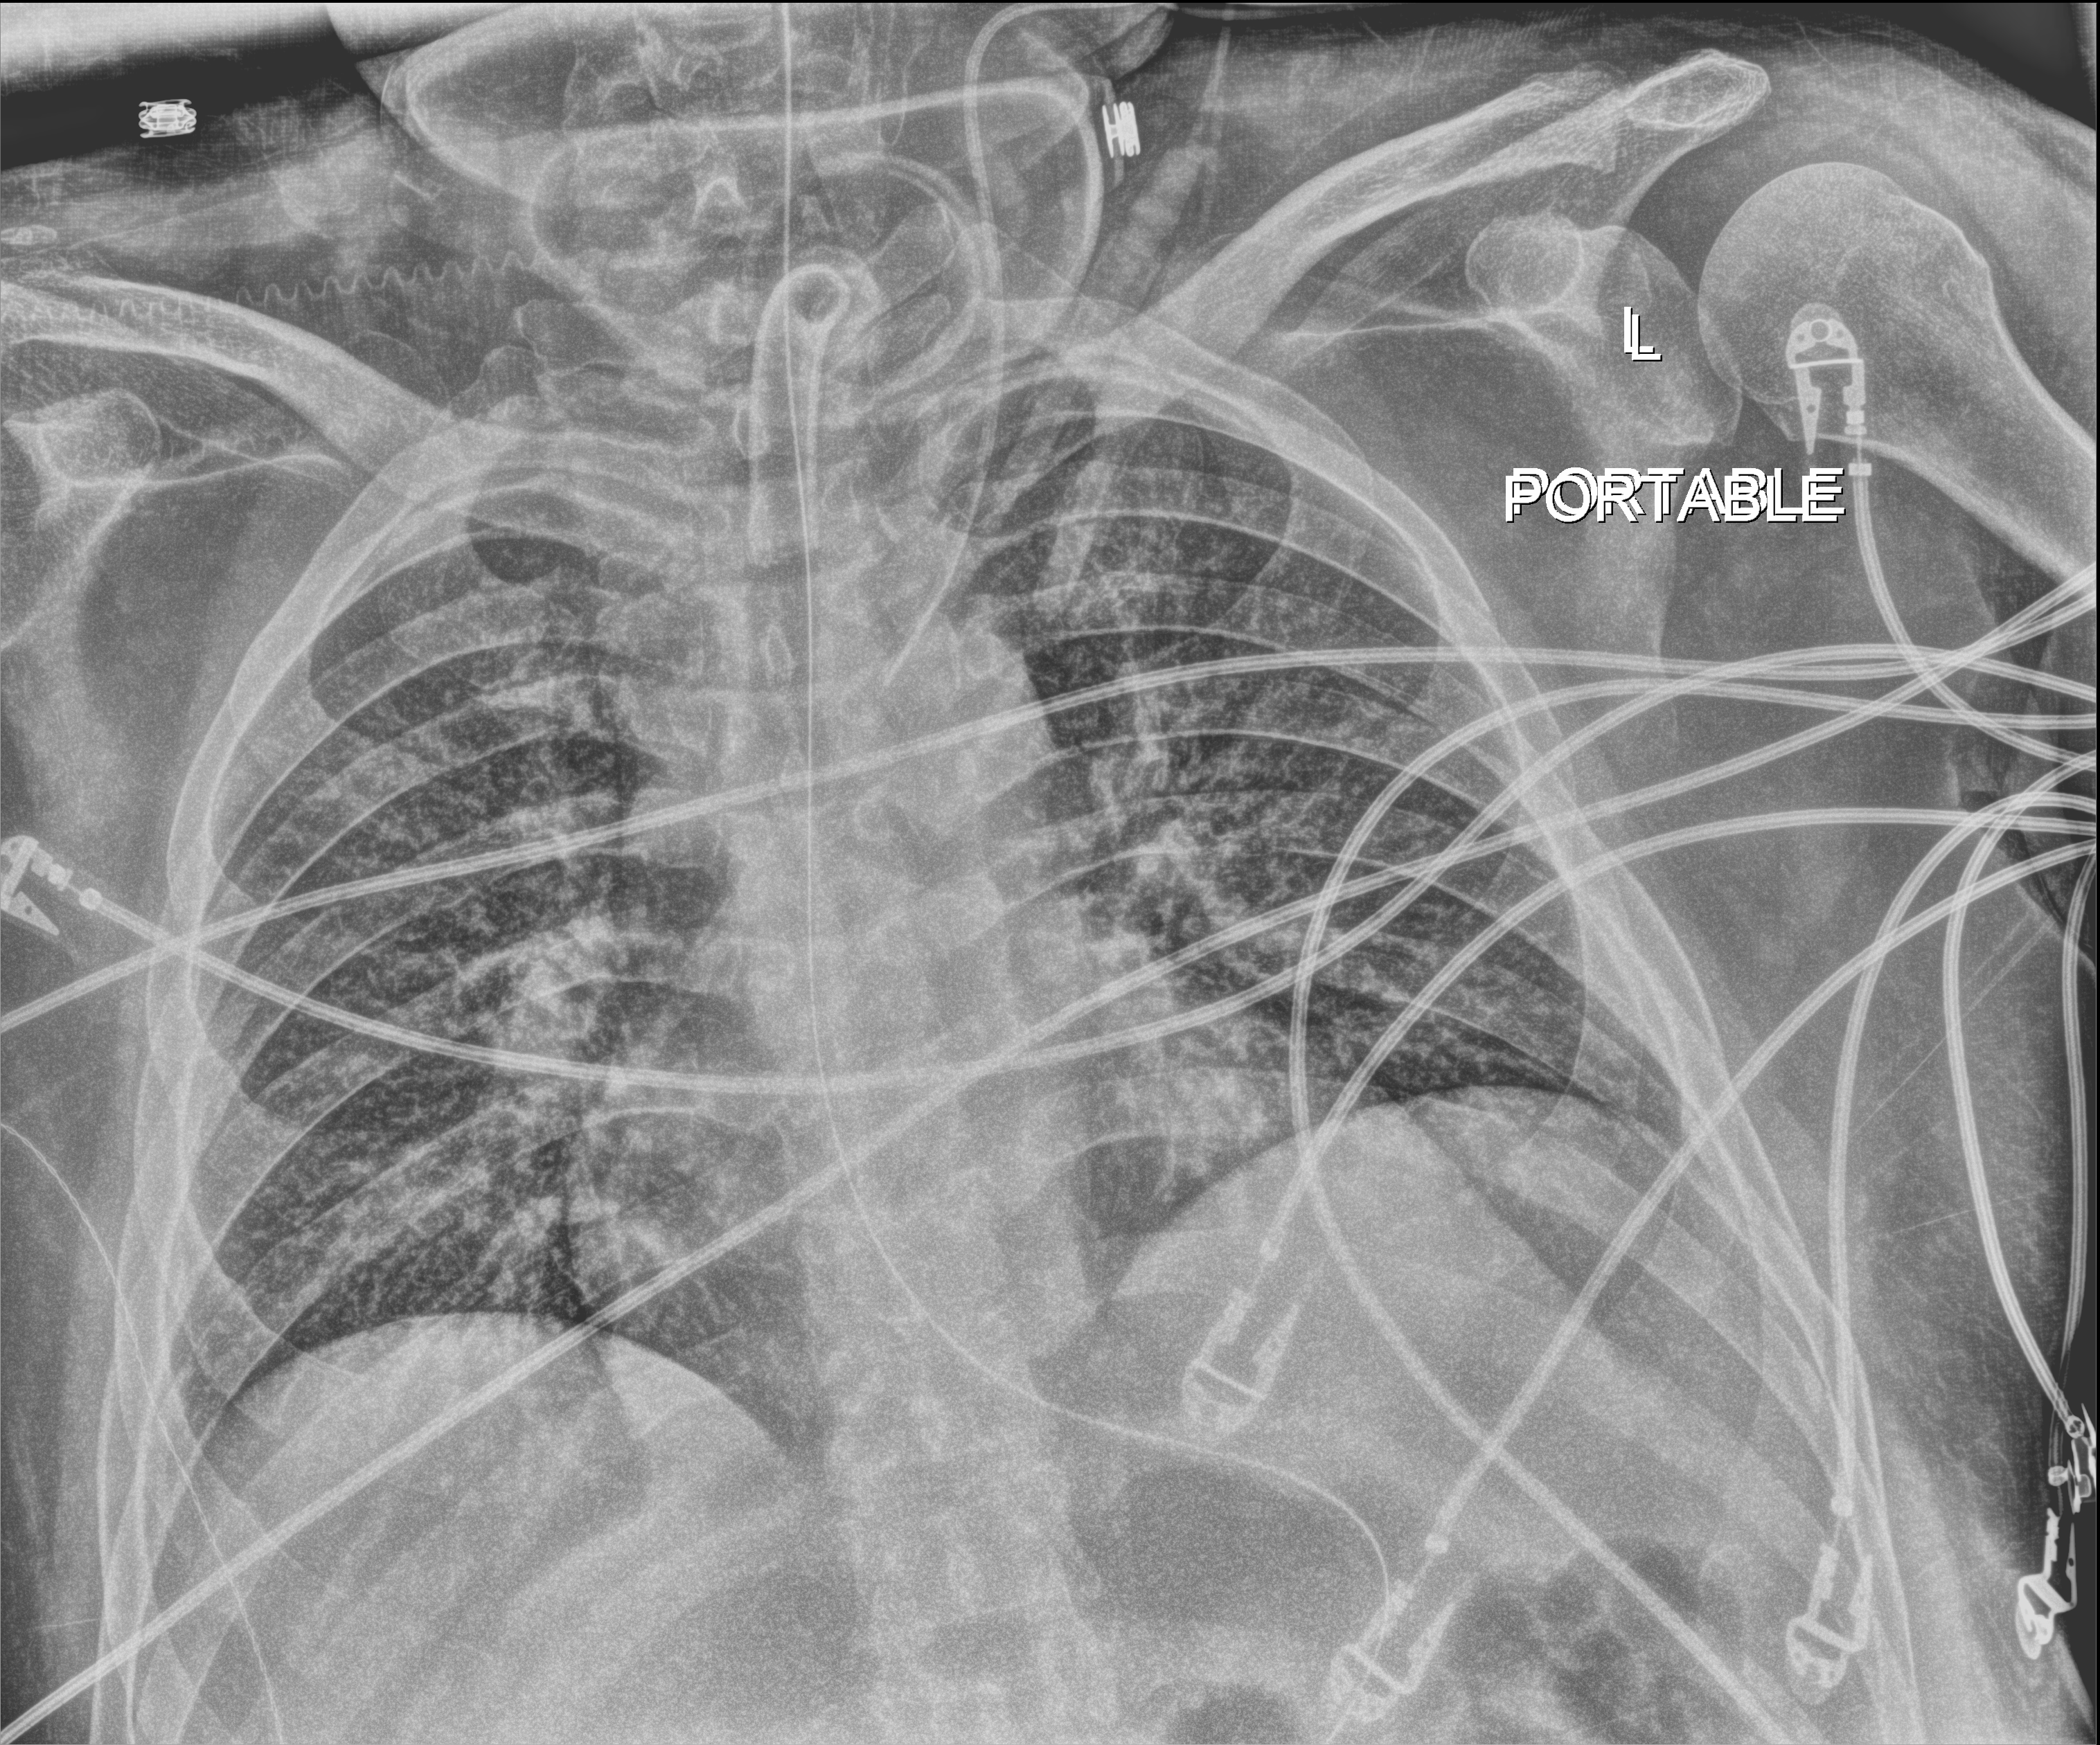
Chest X-ray (portable); anteroposterior (AP) projection. Male patient hospitalised with COVID-19, age 18–59 years.
From the hospital-stay record, not from the radiograph (when in the stay this image was taken is not recorded): mechanically ventilated during this hospital stay: yes.